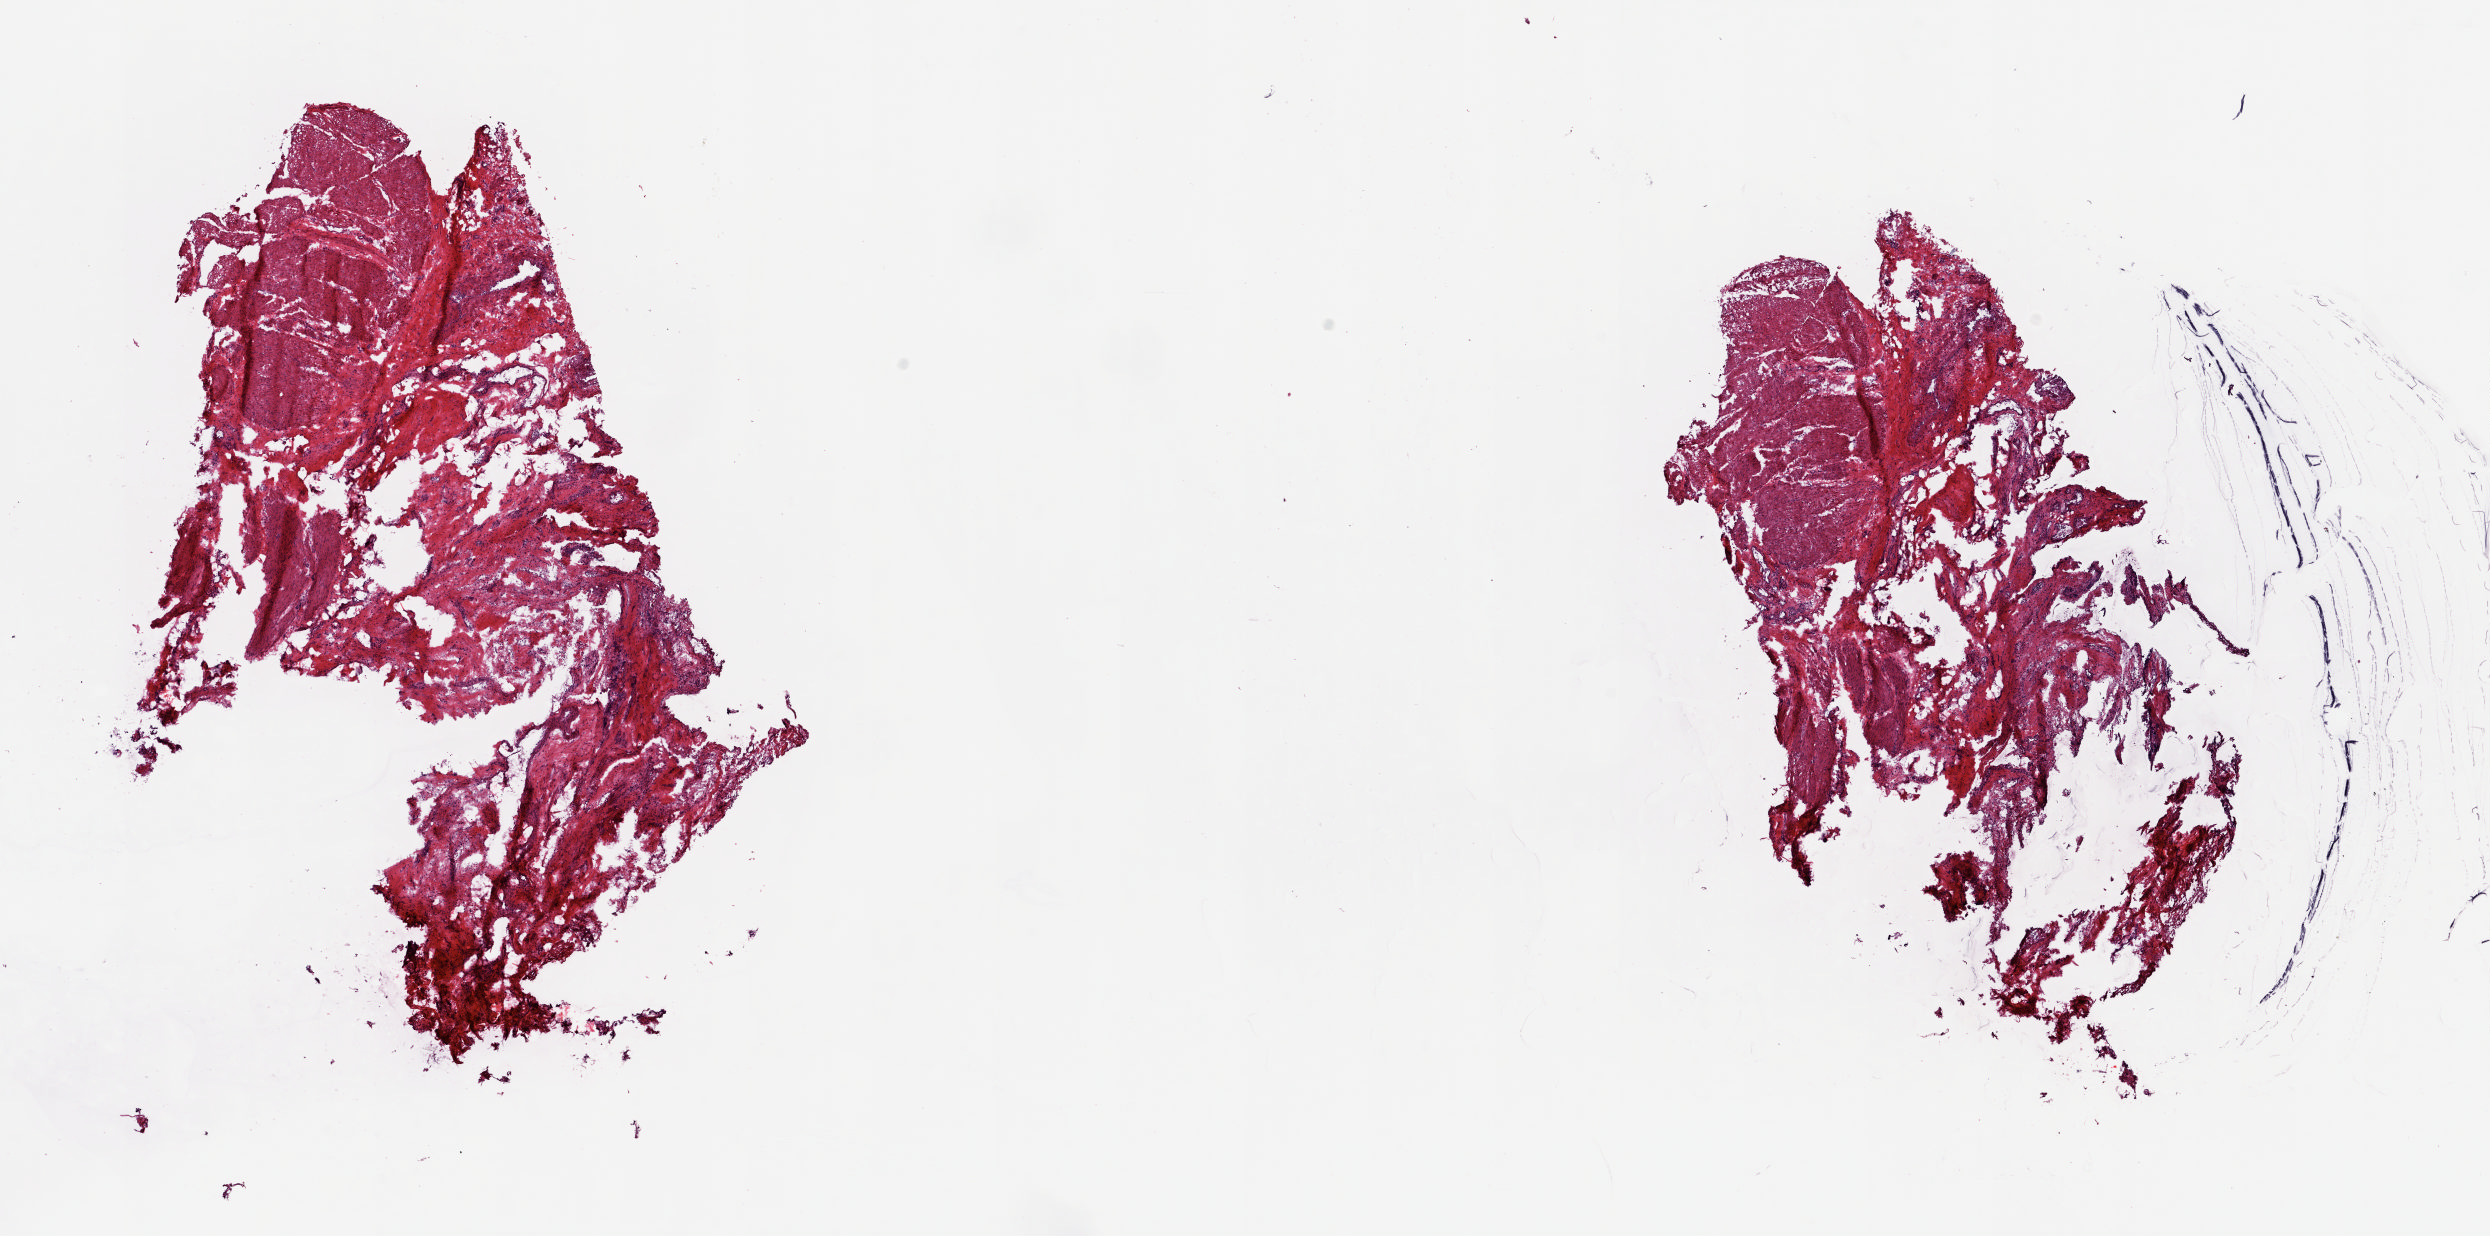
H&E-stained whole-slide image, whole scanned area (about 19.8 x 9.8 mm) shown as a low-resolution overview; frozen section from the top of the tissue portion; sample: solid tissue normal (non-tumour tissue), bladder. Male, age 75 years at initial diagnosis. Pathologist review of this section (percent, as recorded): tumour cells 0%, tumour nuclei 0%, normal cells 0%, stromal cells 100%, necrosis 0%. Inflammatory infiltration, as recorded: lymphocyte infiltration 10%, monocyte infiltration 0%, neutrophil infiltration 0%.
- this section: solid tissue normal (non-tumour) sample from the same patient
- patient diagnosis: Transitional cell carcinoma (lateral wall of bladder)